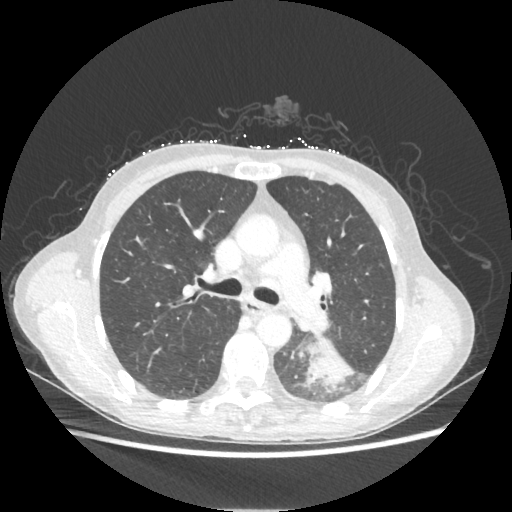
Chest CT, one axial slice. Position 138 of 221 along the scan axis. Reconstruction kernel STANDARD. Lung window (W 1500 / L -600 HU). 1.25 mm slice thickness. 512 × 512 image matrix, field of view 360 × 360 mm. Patient: female, 53 years. From the clinical record (not read from this slice): clinical TNM (as recorded): T3 N0 M0.
Outlined on this slice (rectangle marked by the reading radiologist):
- lung tumour (recorded histology: adenocarcinoma): bounding box (x1, y1, x2, y2) in pixels: (305, 334, 354, 388)